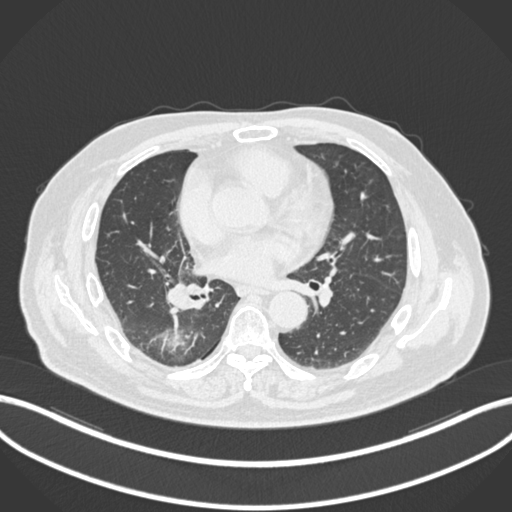
Chest CT, one axial slice; position 89 of 218 along the scan axis; reconstruction kernel B30f; lung window (W 1500 / L -600 HU); 1 mm slice thickness; 512 × 512 image matrix, field of view 400 × 400 mm. Male patient, age 68 years. From the clinical record (not read from this slice): clinical TNM (as recorded): T2a N0 M0.
Outlined on this slice (rectangle marked by the reading radiologist):
- lung tumour (recorded histology: adenocarcinoma): box from (x=146, y=324) to (x=200, y=360) px